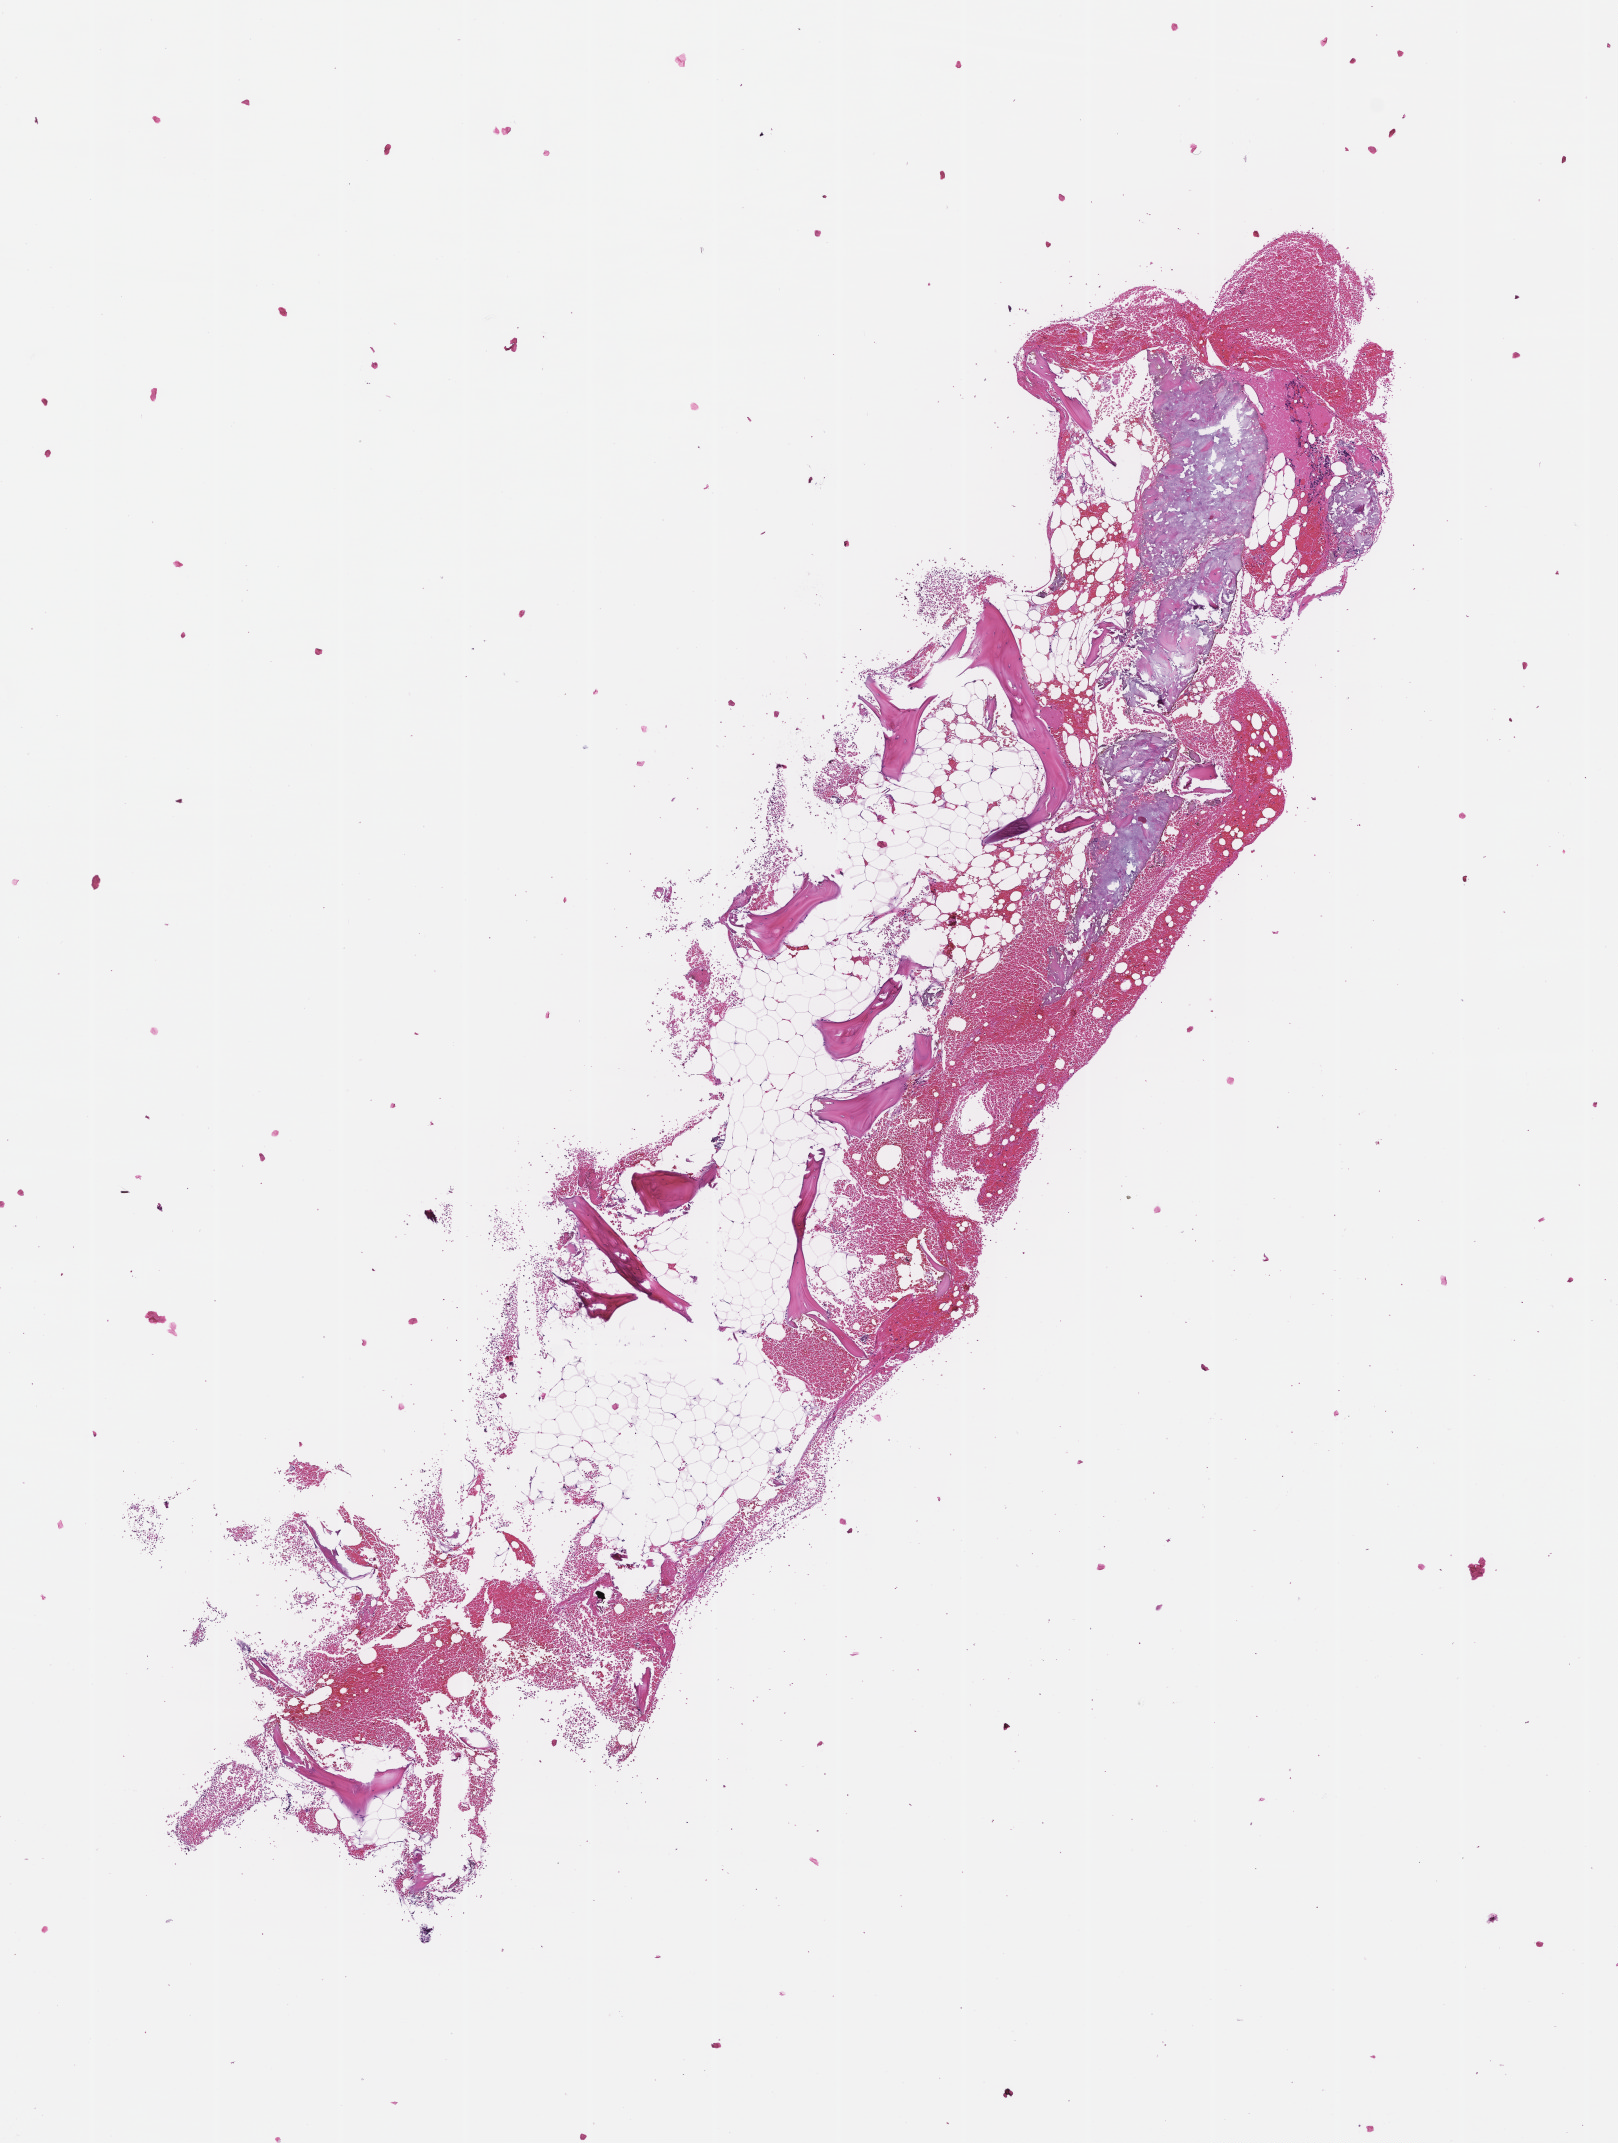
Digitized H&E-stained section — a low-resolution overview of the entire scanned area, about 6.5 x 8.7 mm. FFPE section. Site: bone marrow. Collected on treatment. Patient sex: male.
This section: primary tumor. Diagnosis: Plasma Cell Myeloma.